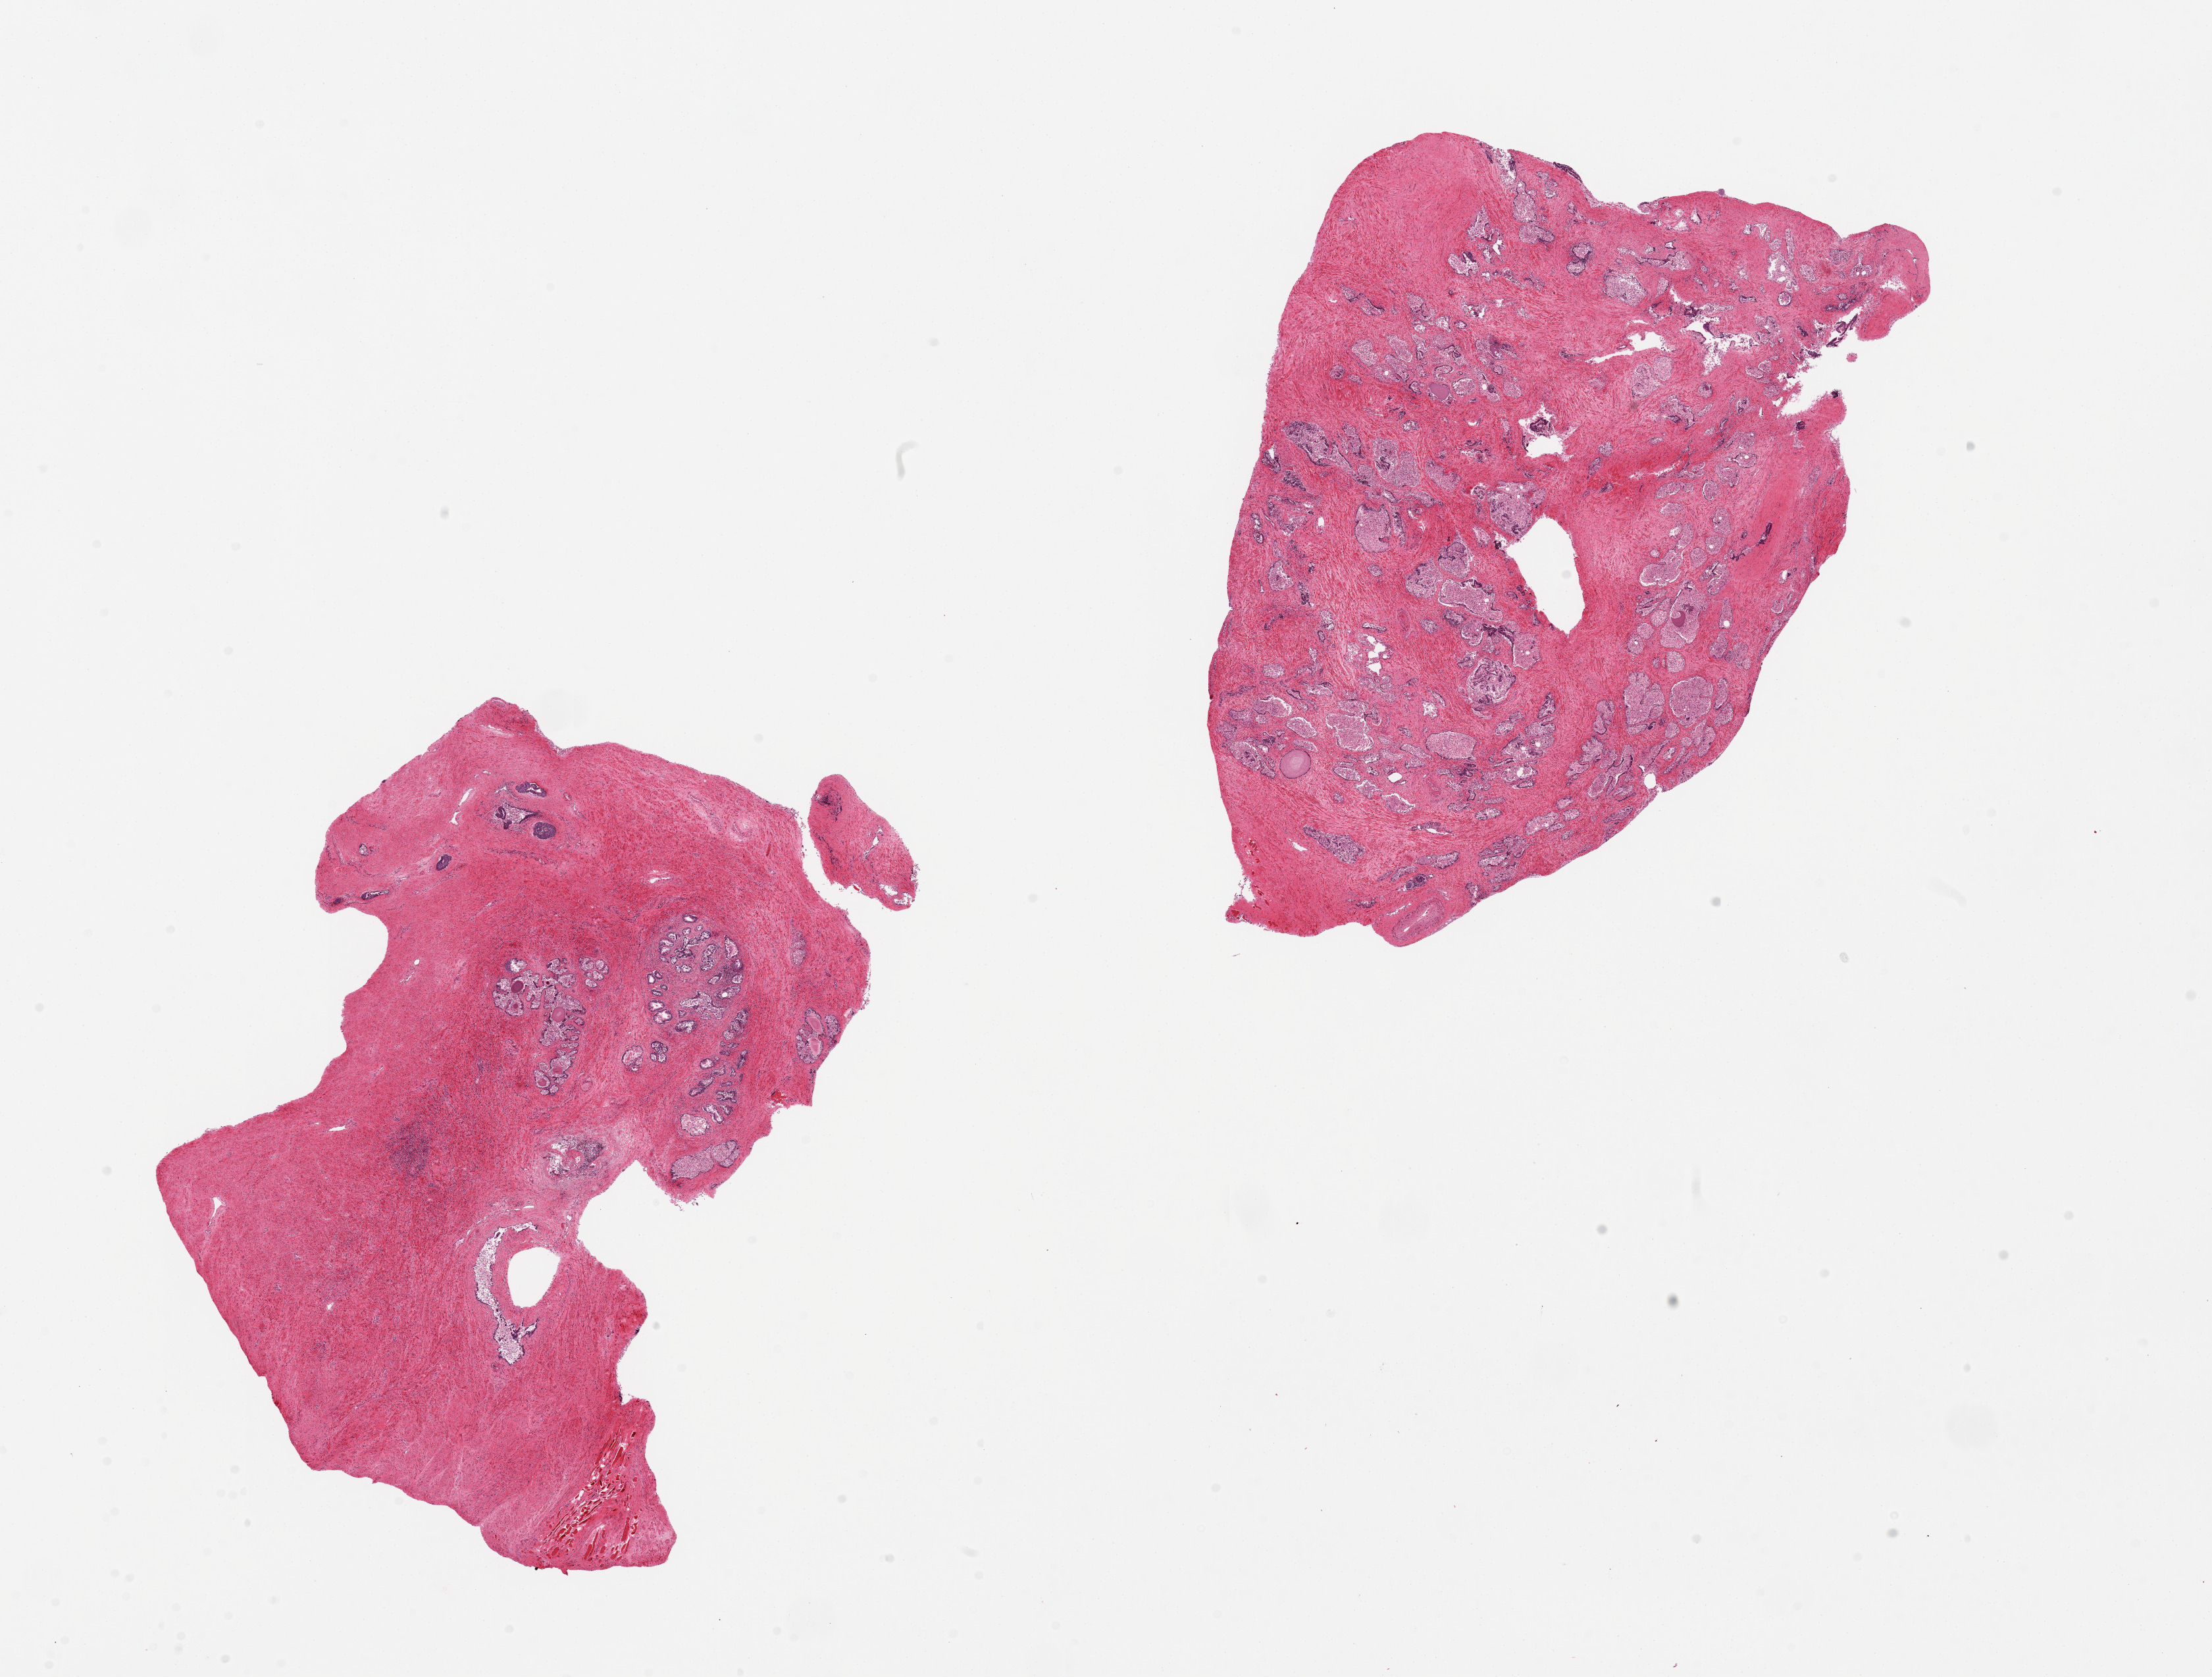
H&E whole-slide image, whole scanned area (about 26.6 x 20.2 mm) shown as a low-resolution overview. PAXgene-fixed paraffin-embedded (PFPE) section. Target tissue: prostate. Donor tissue sample. Donor: male.
Review note (as recorded): 2 pieces; glandular elements moderately/severely autolyzed.